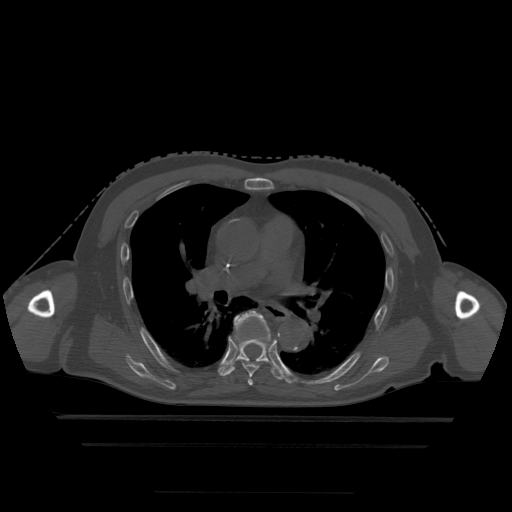
CT including the spine, one axial slice; slice 309 of 522 in the series (ordered by position); bone window (W 1800 / L 400 HU); 512 × 512 image matrix. Patient age 68 years. From the clinical record (not read from this slice): primary cancer: urothelial.
Annotated regions visible in this slice (semi-automatic segmentation, software-assisted and operator-edited):
- T5 vertebra: bounding box <248,376,253,386> (left, top, right, bottom; pixels)
- T6 vertebra: <235,311,269,378>
- T7 vertebra: <220,335,287,380>